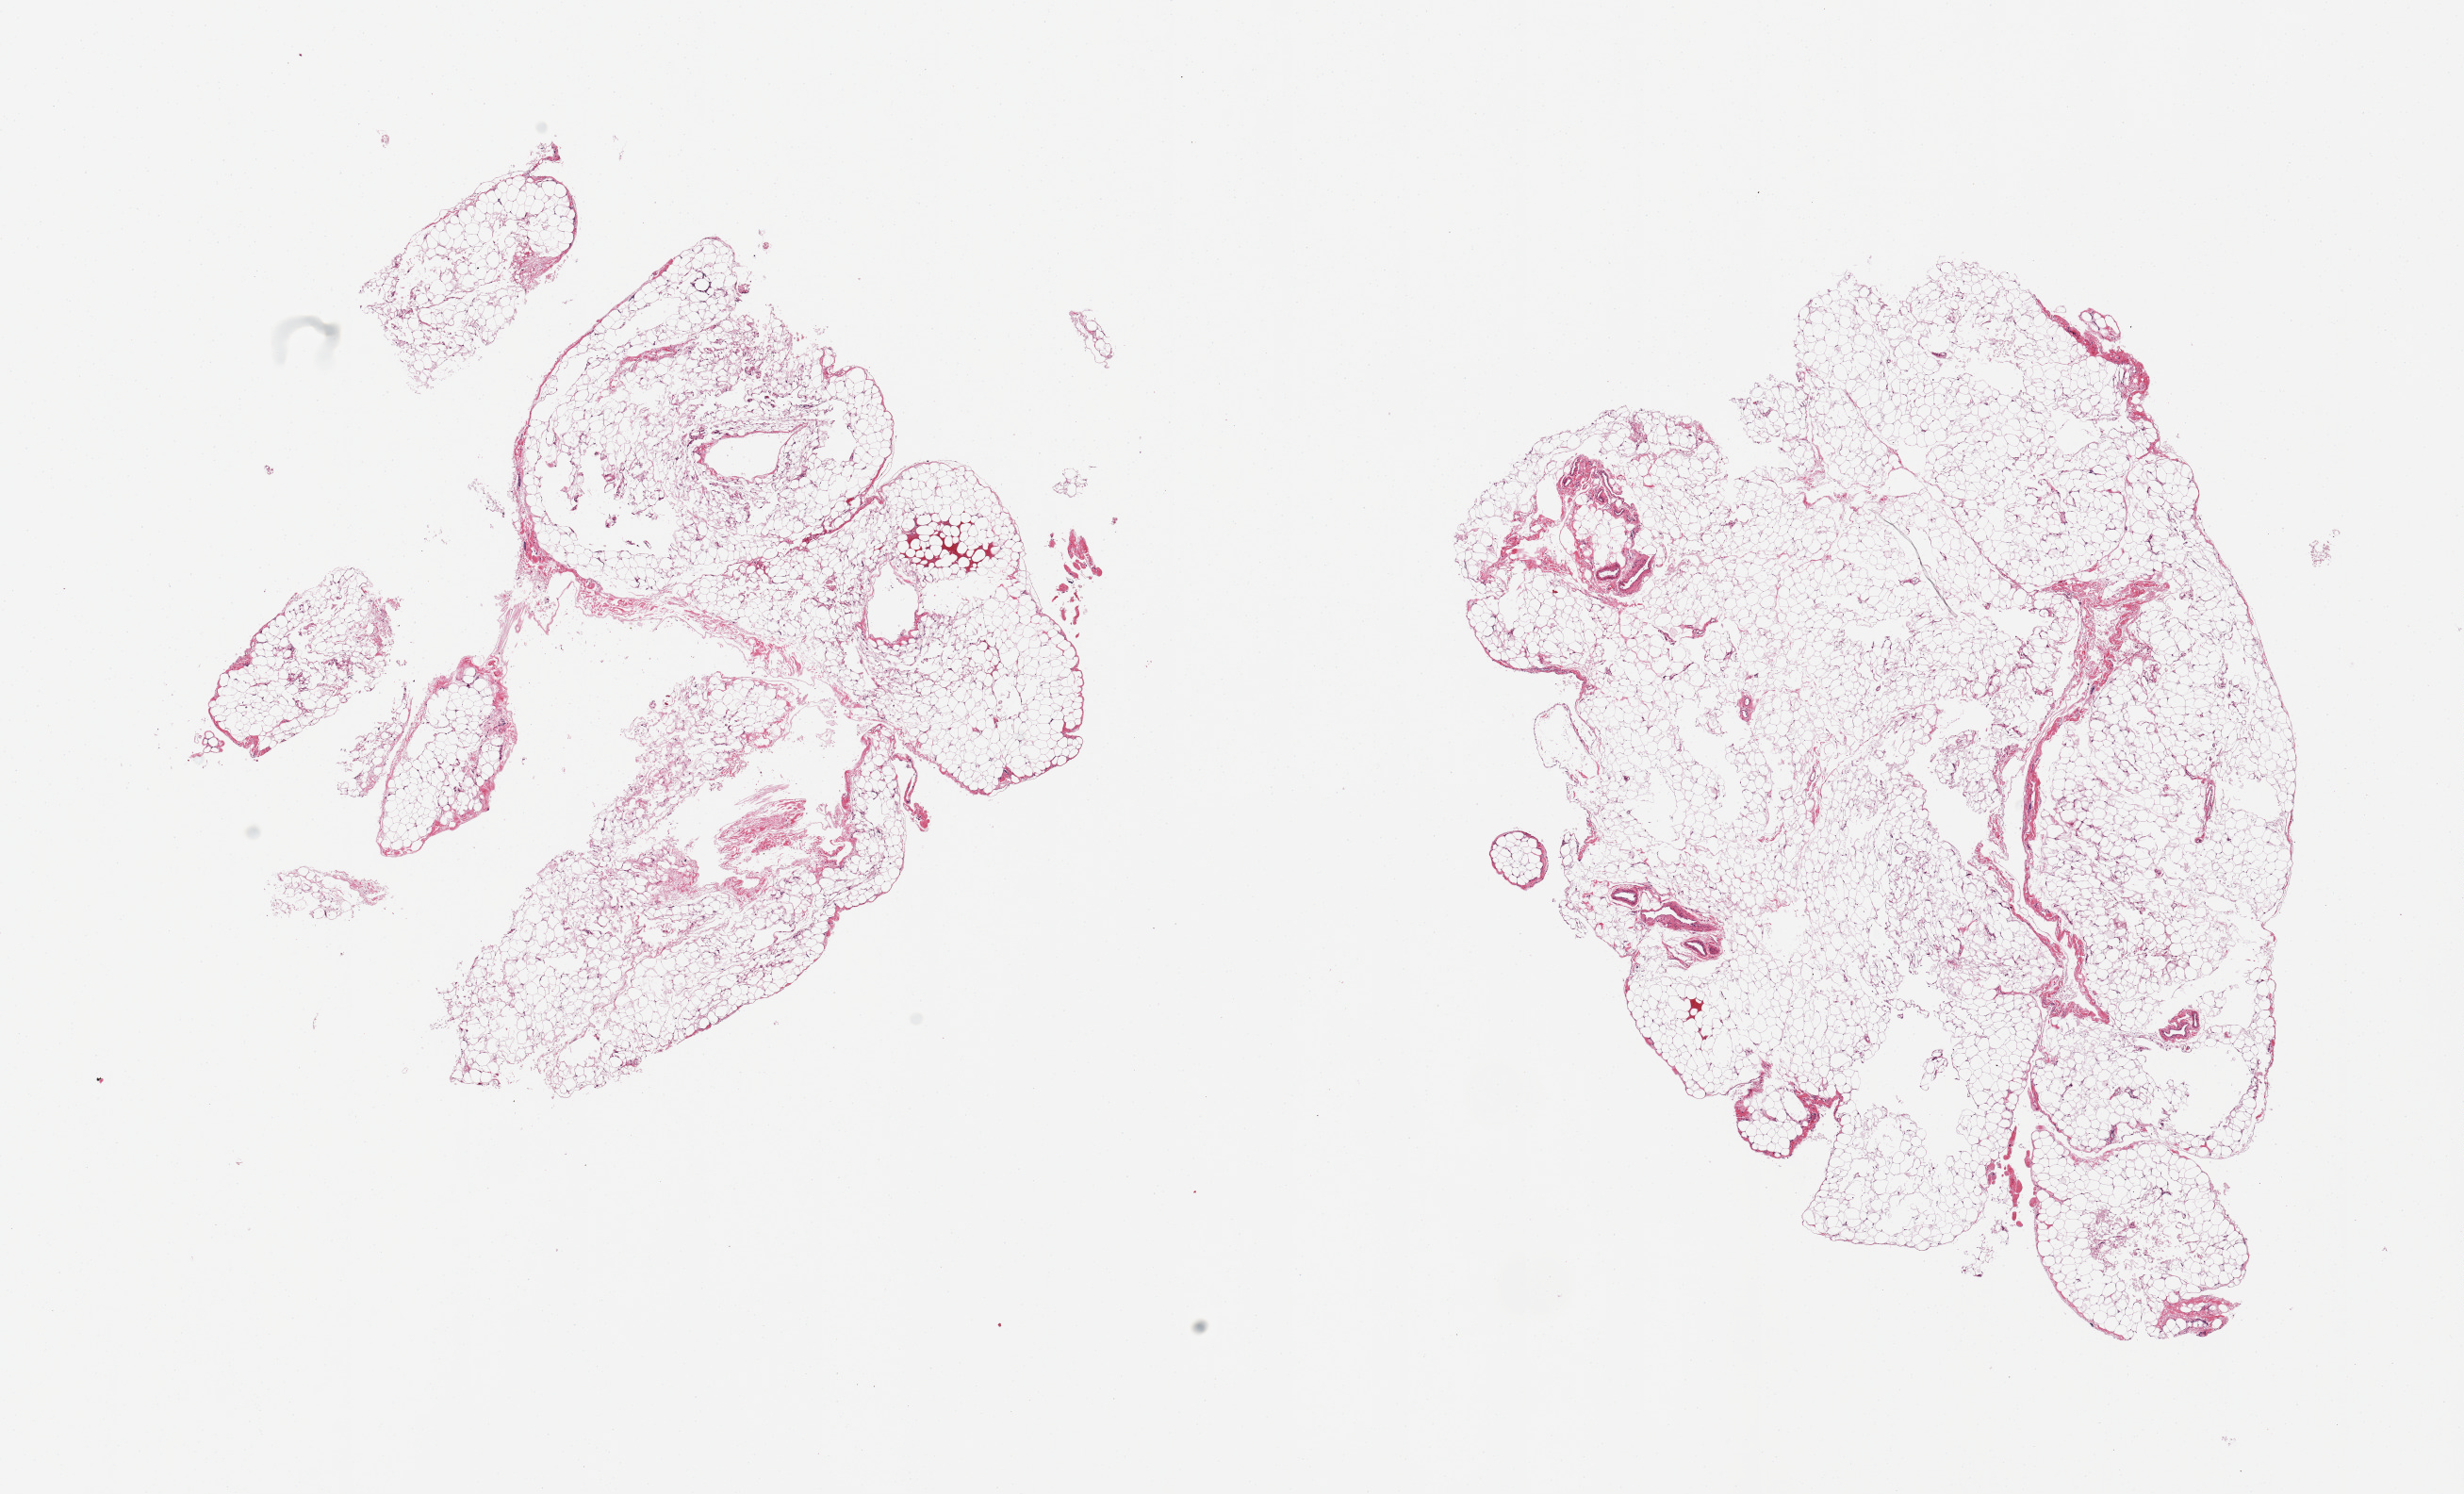
Digitized hematoxylin and eosin (H&E)-stained section — a low-resolution overview of the entire scanned area, about 20.7 x 12.5 mm; PAXgene-fixed paraffin-embedded (PFPE) section; section of omentum (target tissue); tissue donor sample. Donor: female.
Pathologist's review note for this sample: 2 pieces; minimal fibrovascular stroma.